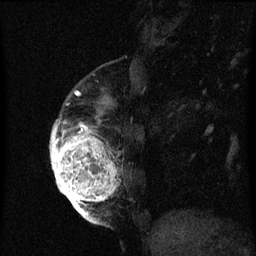
Breast MRI (dynamic contrast-enhanced), one sagittal slice. Slice 16 of 60 in the series (ordered by position). Dynamic contrast-enhanced series, image 2 of 3 at this slice position (ordered by acquisition). 1.5 T. TE 4.2 ms, TR 8 ms. 2 mm slice thickness. 256 × 256 image matrix. Patient: female, 56 years.
Structures marked on this image (semi-automatic segmentation, software-assisted and operator-edited):
- analysis volume of interest (the breast-tissue region the enhancement analysis was run in; not a lesion): bounding box <50,96,121,219> (left, top, right, bottom; pixels)
- tumour enhancement mask (voxels above the 70 % enhancement threshold inside the analysis volume of interest): <50,124,117,219>